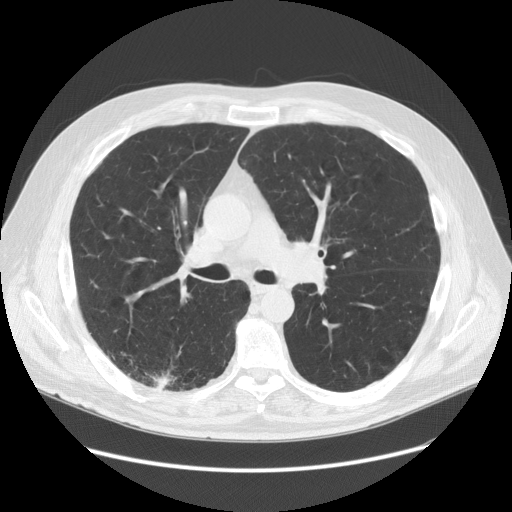
Low-dose screening chest CT, one axial slice; position 88 of 149 along the scan axis; 120 kVp; lung window (W 1500 / L -600 HU); 2.5 mm slice thickness; 512 × 512 image matrix, field of view 400 × 400 mm.
Annotated regions visible in this slice (expert manual segmentation):
- lesion 1 (tumor, lower lobe of right lung): bounding box <151,372,176,391> (left, top, right, bottom; pixels)